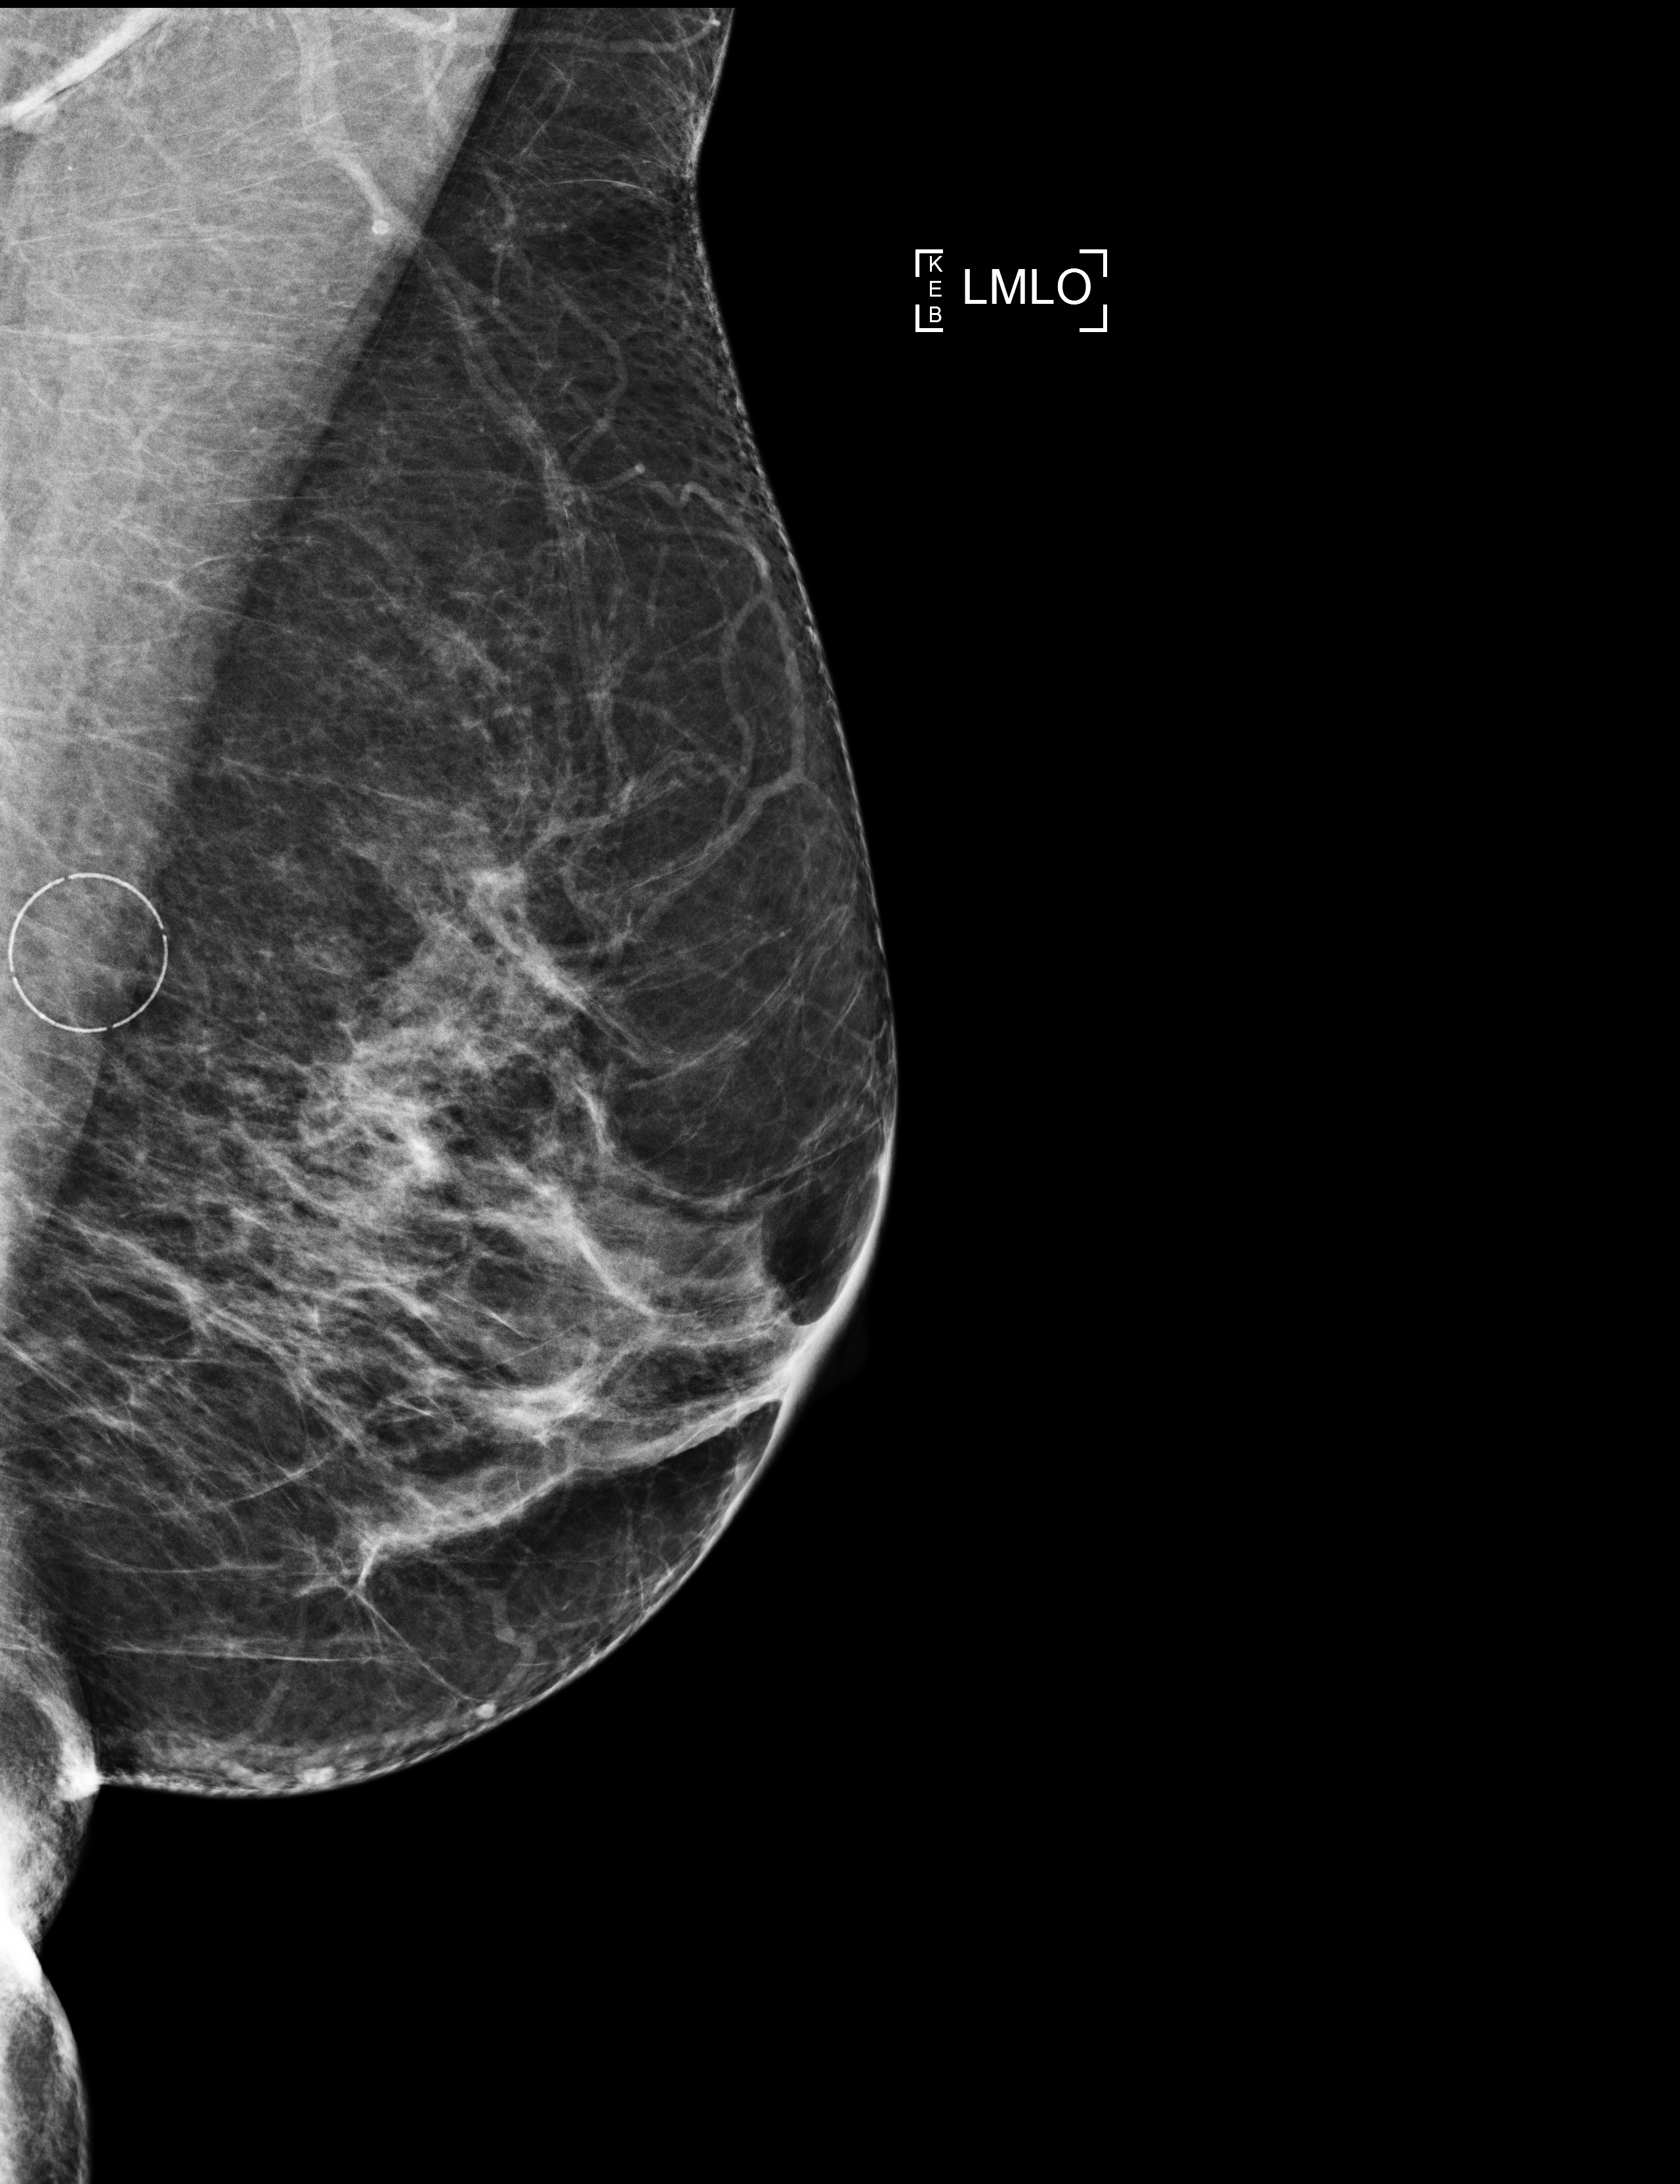
Digital mammogram (FFDM); left breast; medio-lateral oblique projection; annual screening mammography examination; compressed breast thickness 61 mm; system: Selenia Dimensions. Female patient, age 60 years.
Breast density at the screening exam (both breasts): heterogeneously dense (BI-RADS density category c). Final BI-RADS category for the screening round (tomosynthesis exam, both breasts): category 1. Recall: no recall after this screen.